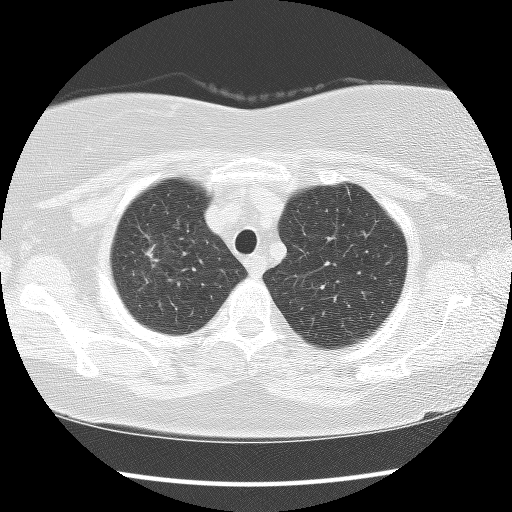
Low-dose screening chest CT, axial slice; second screening round (one year after baseline); lung window (W 1500 / L -600 HU); 2.5 mm slice thickness; lung (sharp) reconstruction kernel (BONE); 120 kVp. Female, age 67 years at enrolment. Former smoker at enrolment.
Lesion marked by an expert reader, box from (x=109, y=226) to (x=166, y=290) px. The screening reader recorded 3 non-calcified nodules or masses ≥4 mm on this exam; which of them this box marks is not recorded. Official screen result: positive, other. Participant outcome: lung cancer diagnosed 56 days after this screen — adenocarcinoma with mixed subtypes, right upper lobe, poorly differentiated (G3), stage IA (AJCC 6th edition), 30 mm at pathology.